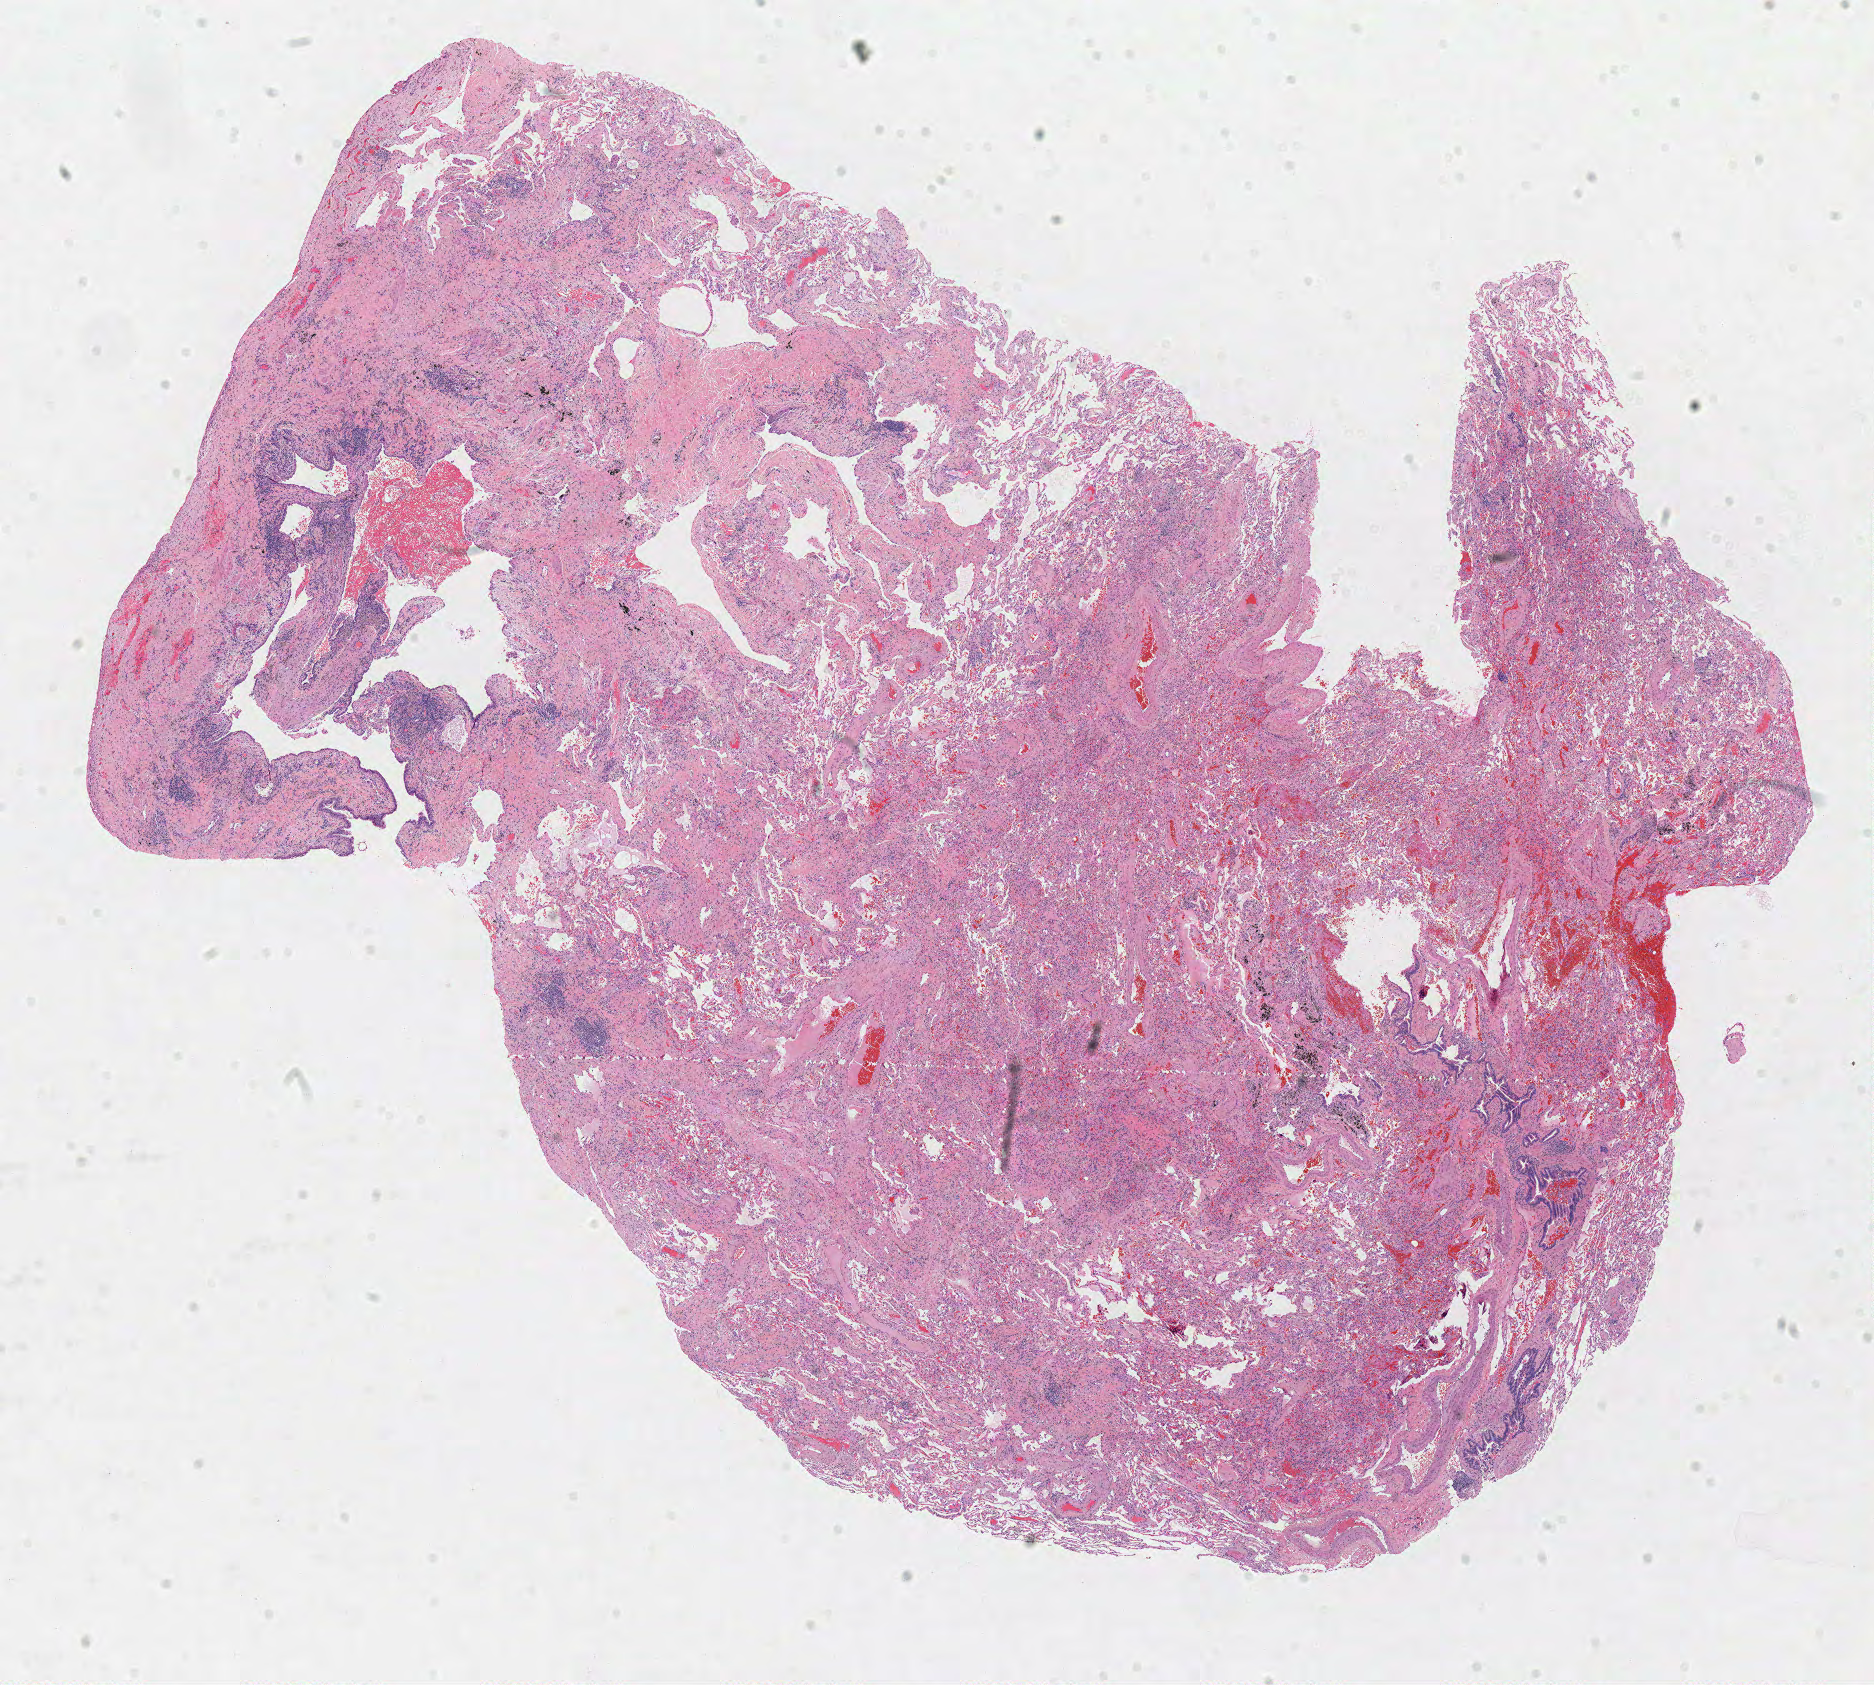
Hematoxylin and eosin (H&E) stained whole-slide image, whole scanned area (about 14.8 x 13.3 mm, from a 40x scan) shown as a low-resolution overview, frozen section from the top of the tissue portion, solid tissue normal (non-tumour tissue) sample from the lung. Male patient; age at initial diagnosis 59 years.
This section: solid tissue normal (non-tumour) sample from the same patient. Patient diagnosis: Adenocarcinoma, NOS.